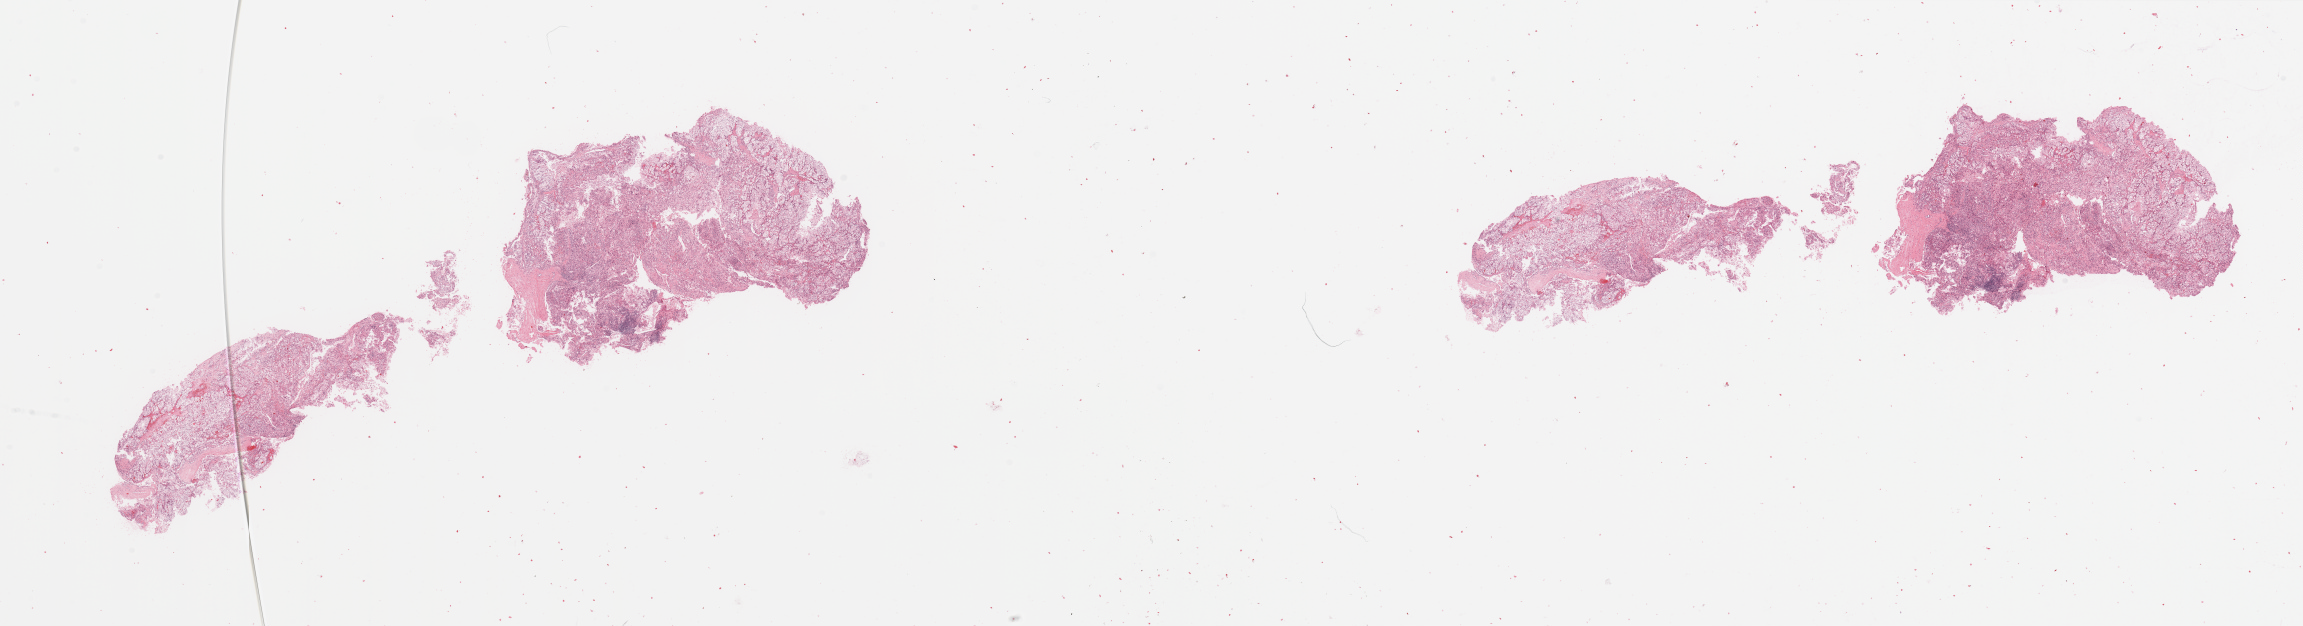
Digitized H&E-stained tissue section (whole slide) — whole scanned area (about 36.4 x 9.9 mm, slide scanned at 20x) shown as a low-resolution overview, tumour tissue sample, sampled site: kidney. Patient: male, age 54 years. Histologic grade: G2 (moderately differentiated). Composition of this section per pathologist review: tumour nuclei 85%, necrosis 2%.
Primary tumour site (as recorded): middle. Diagnosis: Renal cell carcinoma, NOS. AJCC pathologic stage: I.